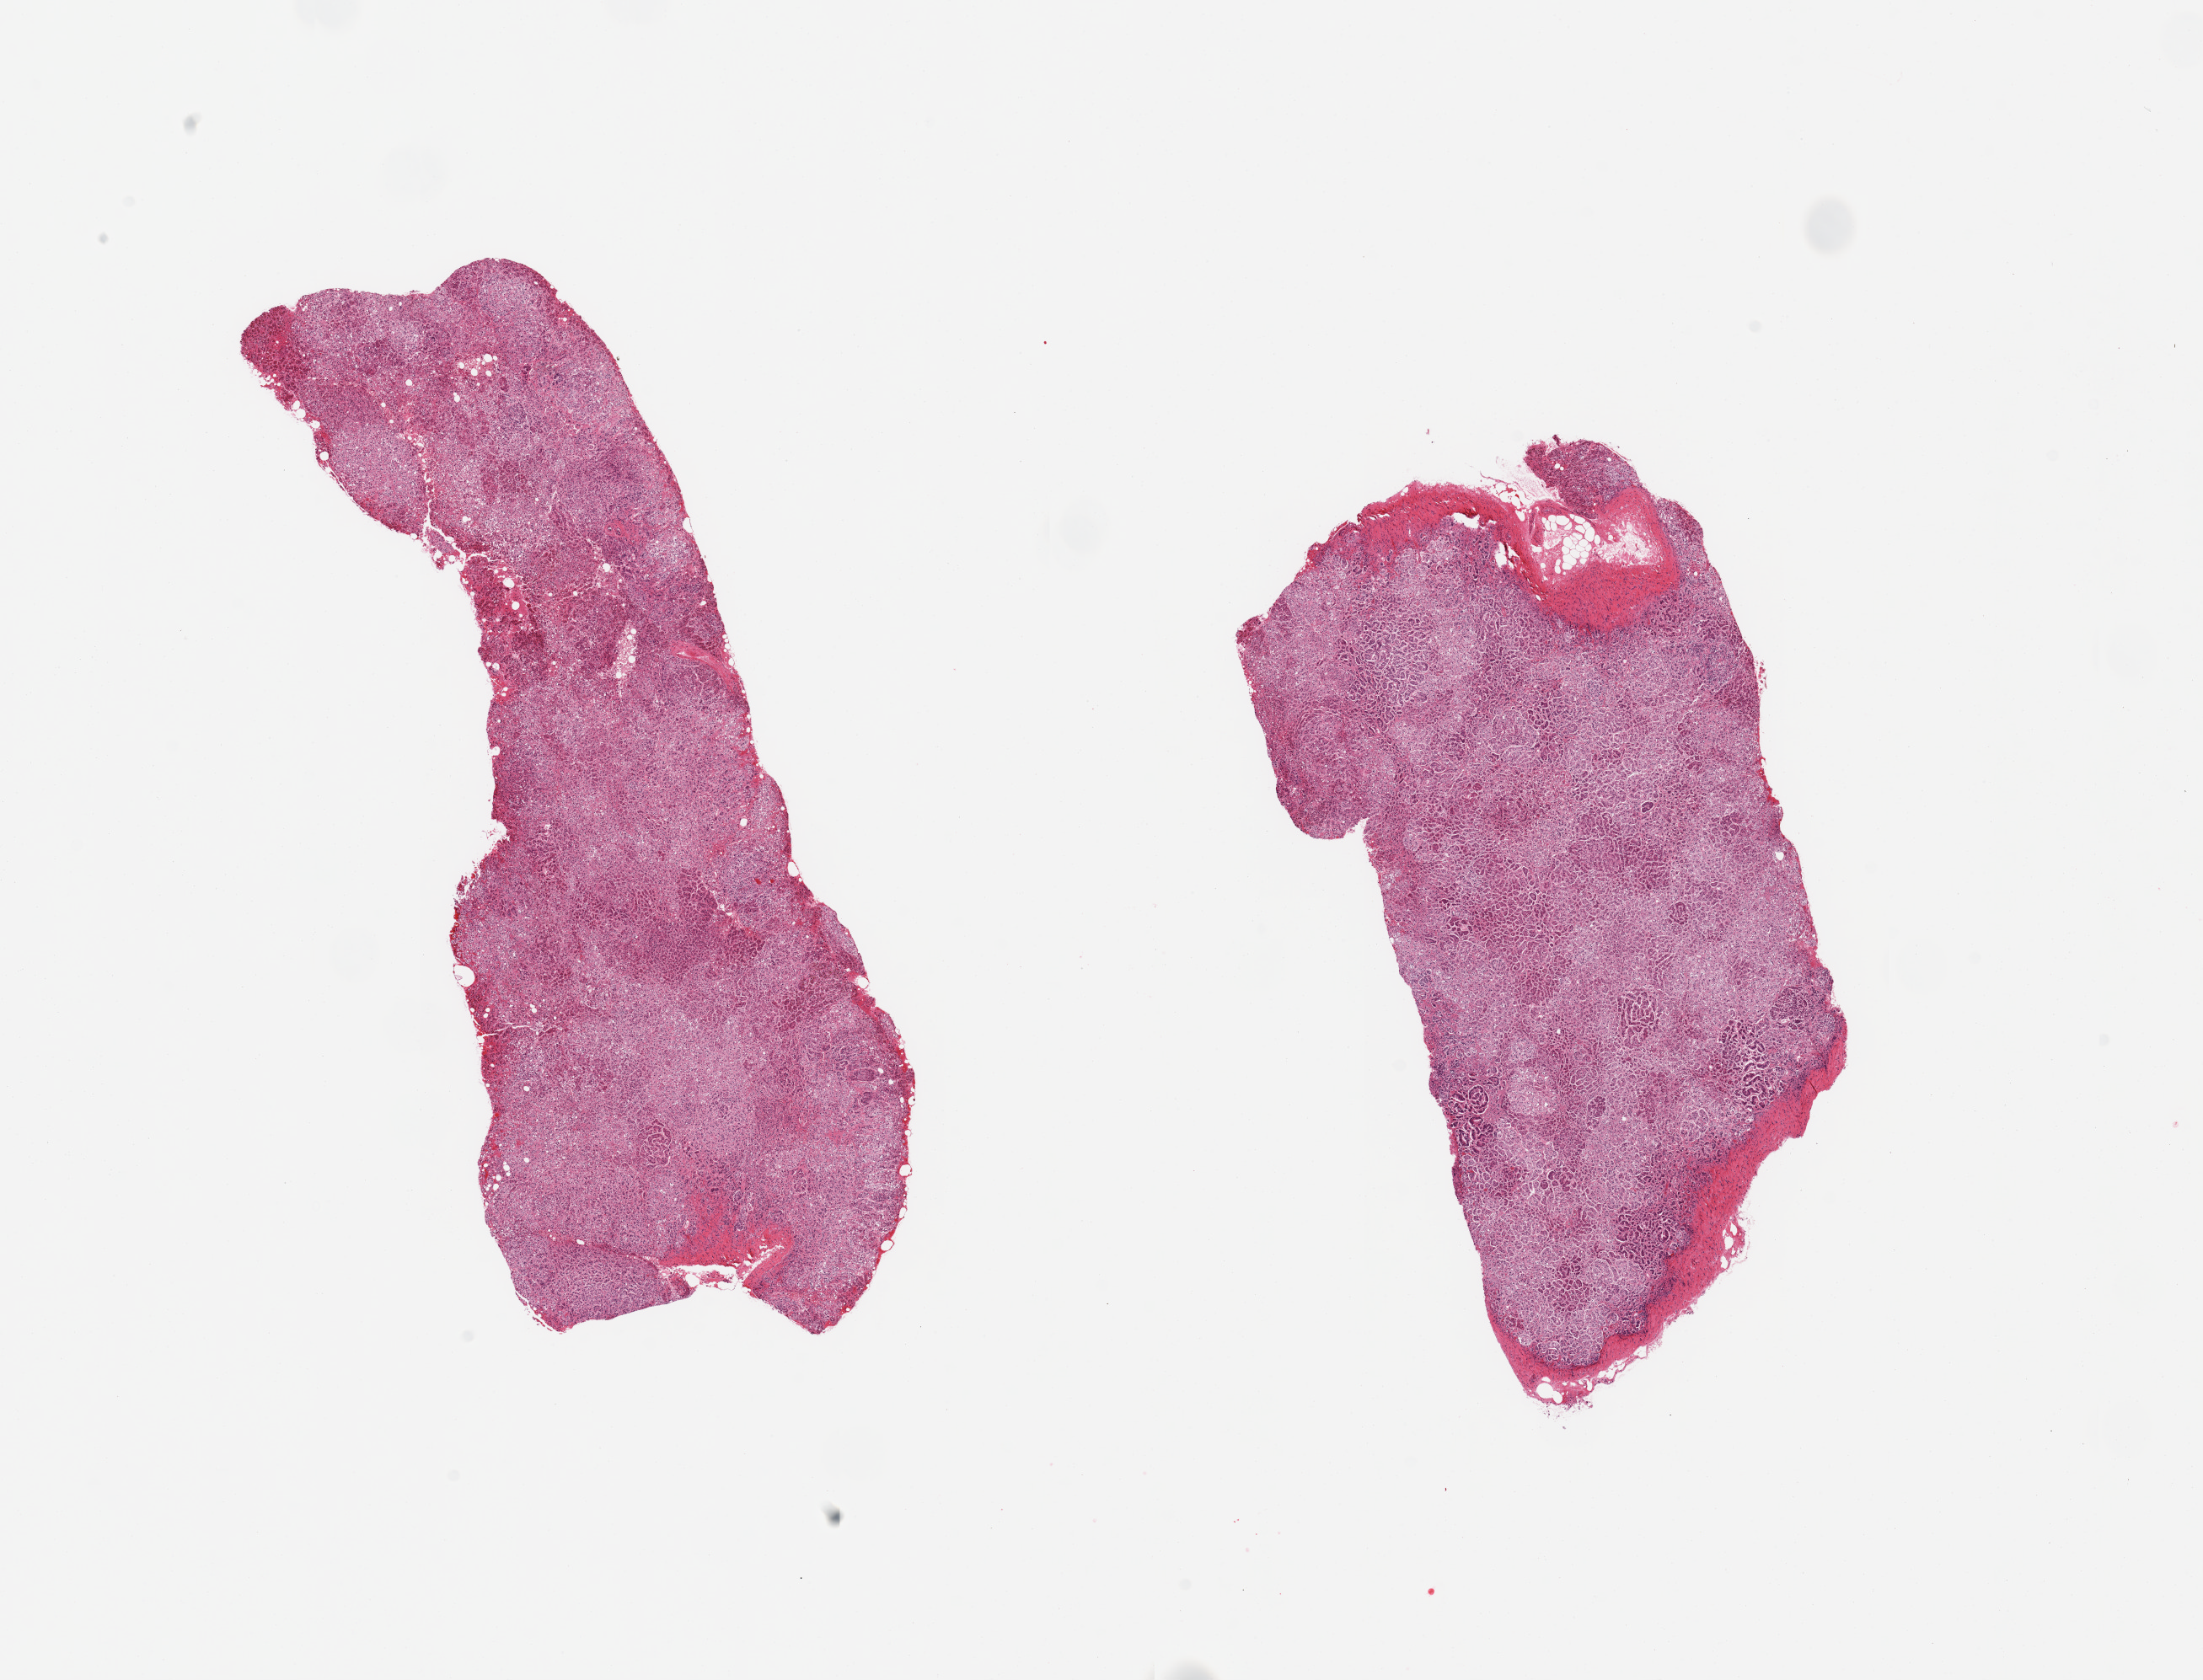
Digitized H&E-stained section, low-resolution overview of the scanned area, about 20.7 x 15.8 mm (slide scanned at 20x); PAXgene-fixed paraffin-embedded (PFPE) section; sampled site (target tissue): adrenal gland; donor tissue sample. Donor sex: male.
Reviewer comment on this tissue sample: 2 pieces; well trimmed.